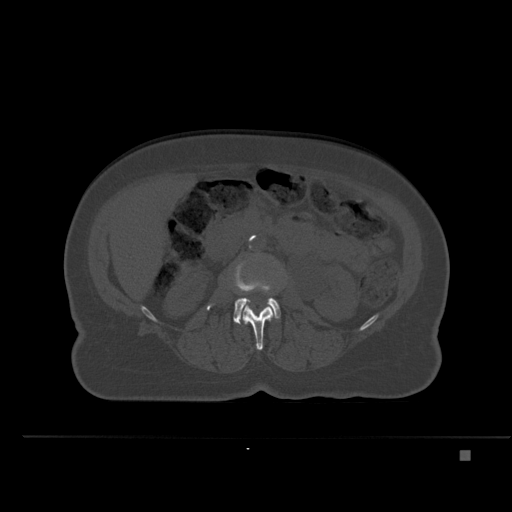
CT including the spine, one axial slice; position 208 of 477 along the scan axis; bone window (W 1800 / L 400 HU); 1.5 mm slice thickness; 512 × 512 image matrix, field of view 422 × 422 mm. Female patient, age 74 years. From the clinical record (not read from this slice): primary cancer: colon.
Annotated regions visible in this slice (semi-automatically segmented with operator editing):
- L2 vertebra: bounding box <243,304,273,351> (left, top, right, bottom; pixels)
- L3 vertebra: <207,265,280,324>